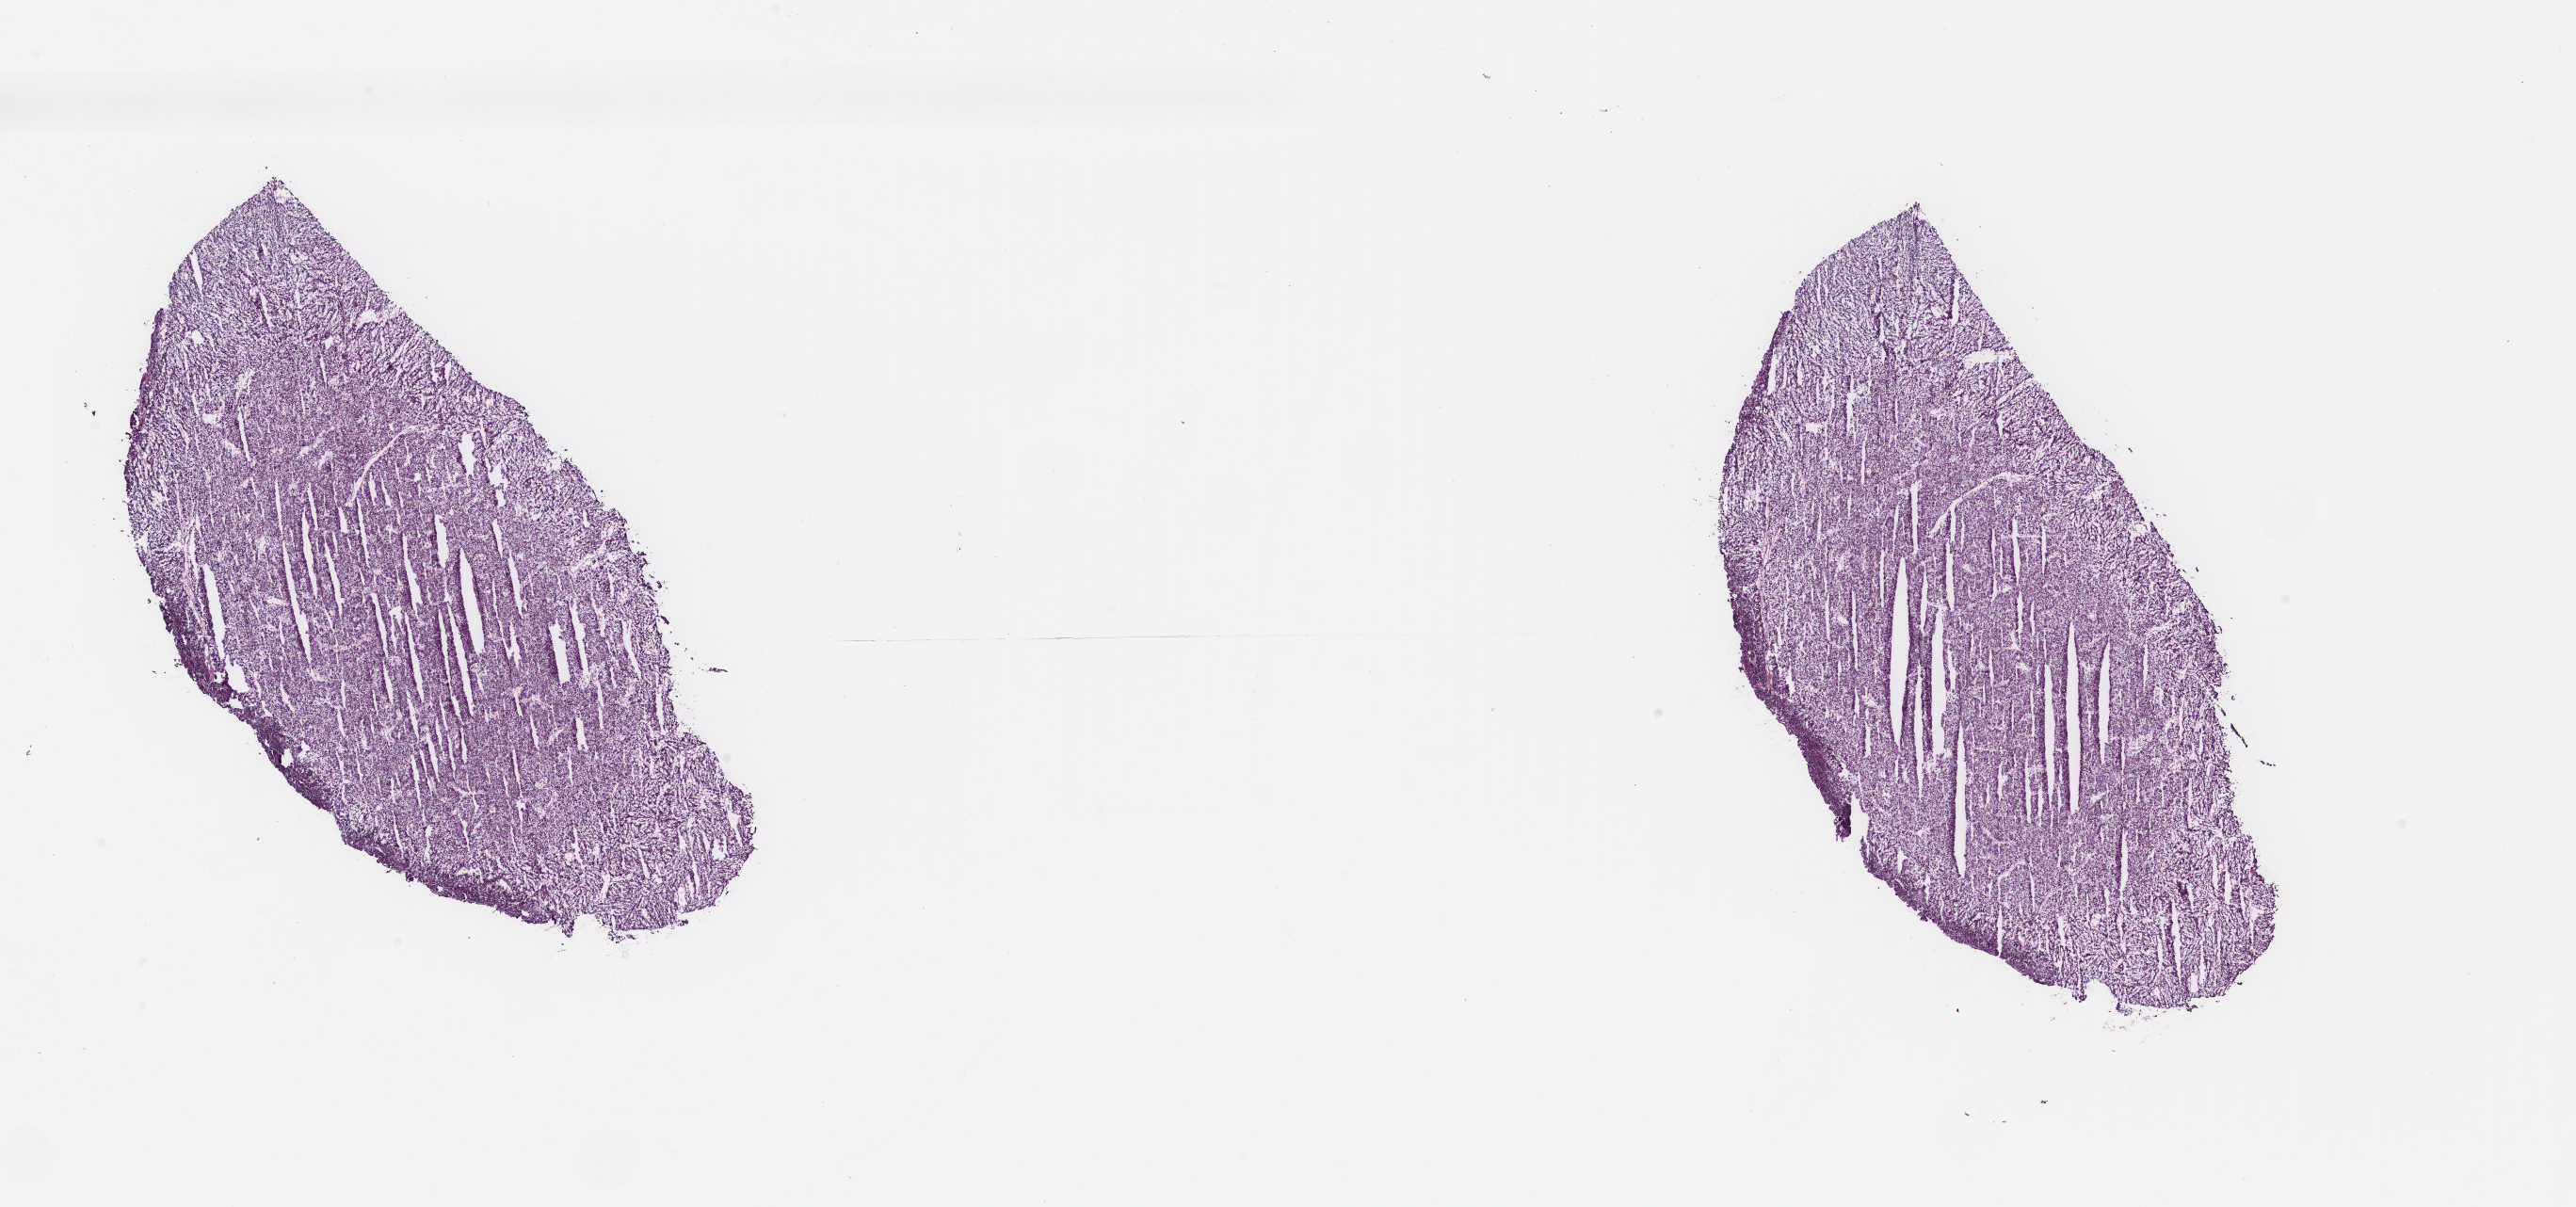
Whole-slide histology image, H&E, shown as a low-resolution overview of the whole scanned area (about 21.7 x 10.2 mm); frozen section from the top of the tissue portion; primary tumour sample from the liver. Patient: male, age at initial diagnosis 65 years. Histologic grade: G2 (moderately differentiated). Composition of this section per pathologist review: tumour cells 100%, tumour nuclei 90%, normal cells 0%, stromal cells 0%, necrosis 0%. Infiltration values recorded for this section: lymphocyte infiltration 1%, monocyte infiltration 0%, neutrophil infiltration 1%.
AJCC pathologic stage: IIIA (5th edition). Diagnosis: Hepatocellular carcinoma, NOS.